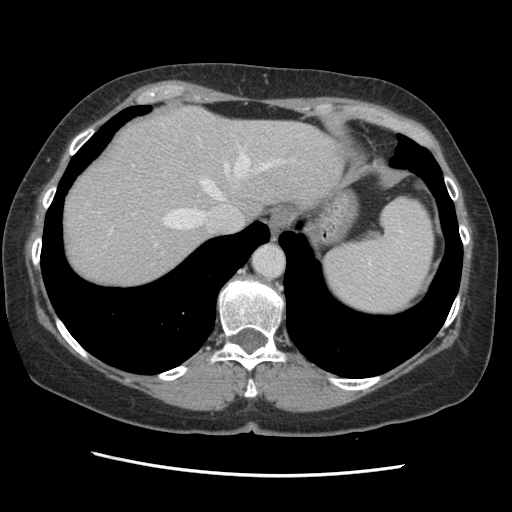
Contrast-enhanced abdominal CT, one axial slice; position 114 of 141 along the scan axis; soft-tissue window (W 400 / L 40 HU); 2.5 mm slice thickness; 512 × 512 image matrix. Female patient, age 61 years. From the clinical record (not read from this slice): diagnosis: colorectal cancer liver metastases, imaged before liver resection; multiple liver metastases: no; largest metastasis: 2.4 cm.
Structures marked on this image (manually delineated by an expert):
- hepatic veins: box from (x=132, y=135) to (x=295, y=247) px
- liver: (x=63, y=105)–(x=343, y=289)
- planned liver remnant (the part of the liver to remain after resection): (x=63, y=105)–(x=343, y=288)
- portal vein (with intrahepatic branches): (x=110, y=228)–(x=163, y=254)